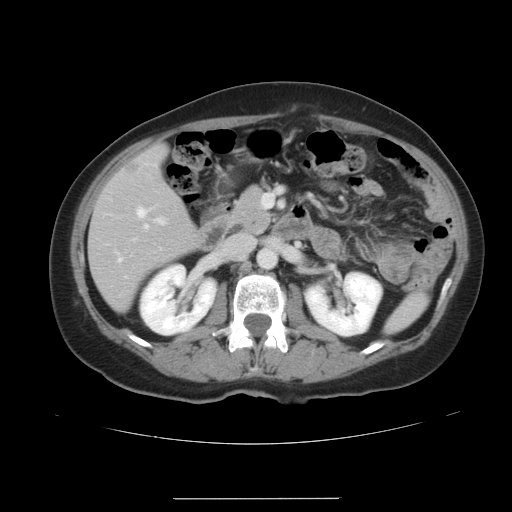
Contrast-enhanced abdominal CT, one axial slice; slice 17 of 41 in the series (ordered by position); intravenous contrast given; soft-tissue window (W 400 / L 40 HU); 5 mm slice thickness; 512 × 512 image matrix, field of view 381 × 381 mm. Female patient, age 63 years. Case-level facts recorded for this patient, not image findings: diagnosis: colorectal cancer liver metastases, imaged before liver resection; multiple liver metastases: yes.
Annotated regions visible in this slice (manually delineated by an expert):
- hepatic veins: bounding box (x1, y1, x2, y2) in pixels: (118, 208, 147, 261)
- liver: (90, 147, 200, 309)
- planned liver remnant (the part of the liver to remain after resection): (90, 148, 200, 309)
- portal vein (with intrahepatic branches): (156, 218, 164, 223)
- liver metastasis: (125, 162, 139, 175)